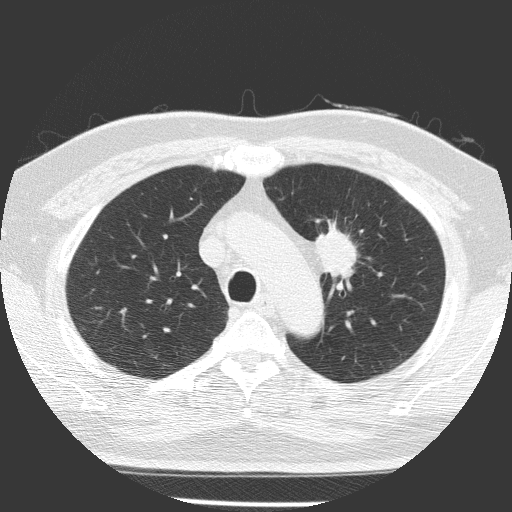
Low-dose screening chest CT, axial slice, baseline screening round, lung window (W 1500 / L -600 HU), 2 mm slice thickness, 120 kVp. Male, age 70 years at enrolment. Current smoker at enrolment.
Expert-annotated lung lesion, bounding box <298,222,372,296> (left, top, right, bottom; pixels). The screening reader recorded 3 non-calcified nodules or masses ≥4 mm on this exam (left upper lobe, left lower lobe, left upper lobe); which of them this box marks is not recorded. Lung cancer was diagnosed 58 days after this screen: squamous cell carcinoma, NOS, left upper lobe, poorly differentiated (G3), stage IB (AJCC 6th edition), 47 mm at pathology.